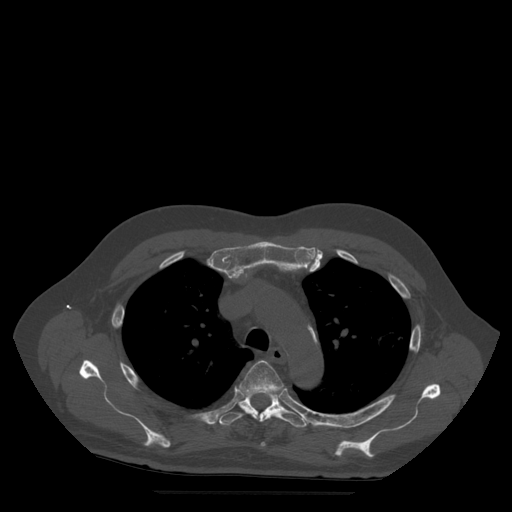
CT including the spine, one axial slice. Position 382 of 522 along the scan axis. Bone window (W 1800 / L 400 HU). 512 × 512 image matrix, field of view 420 × 420 mm. Patient age 72 years. From the clinical record (not read from this slice): primary cancer: prostate.
Outlined on this slice (semi-automatically segmented with operator editing):
- T4 vertebra: bounding box <240,361,284,446> (left, top, right, bottom; pixels)
- T5 vertebra: <219,394,308,427>